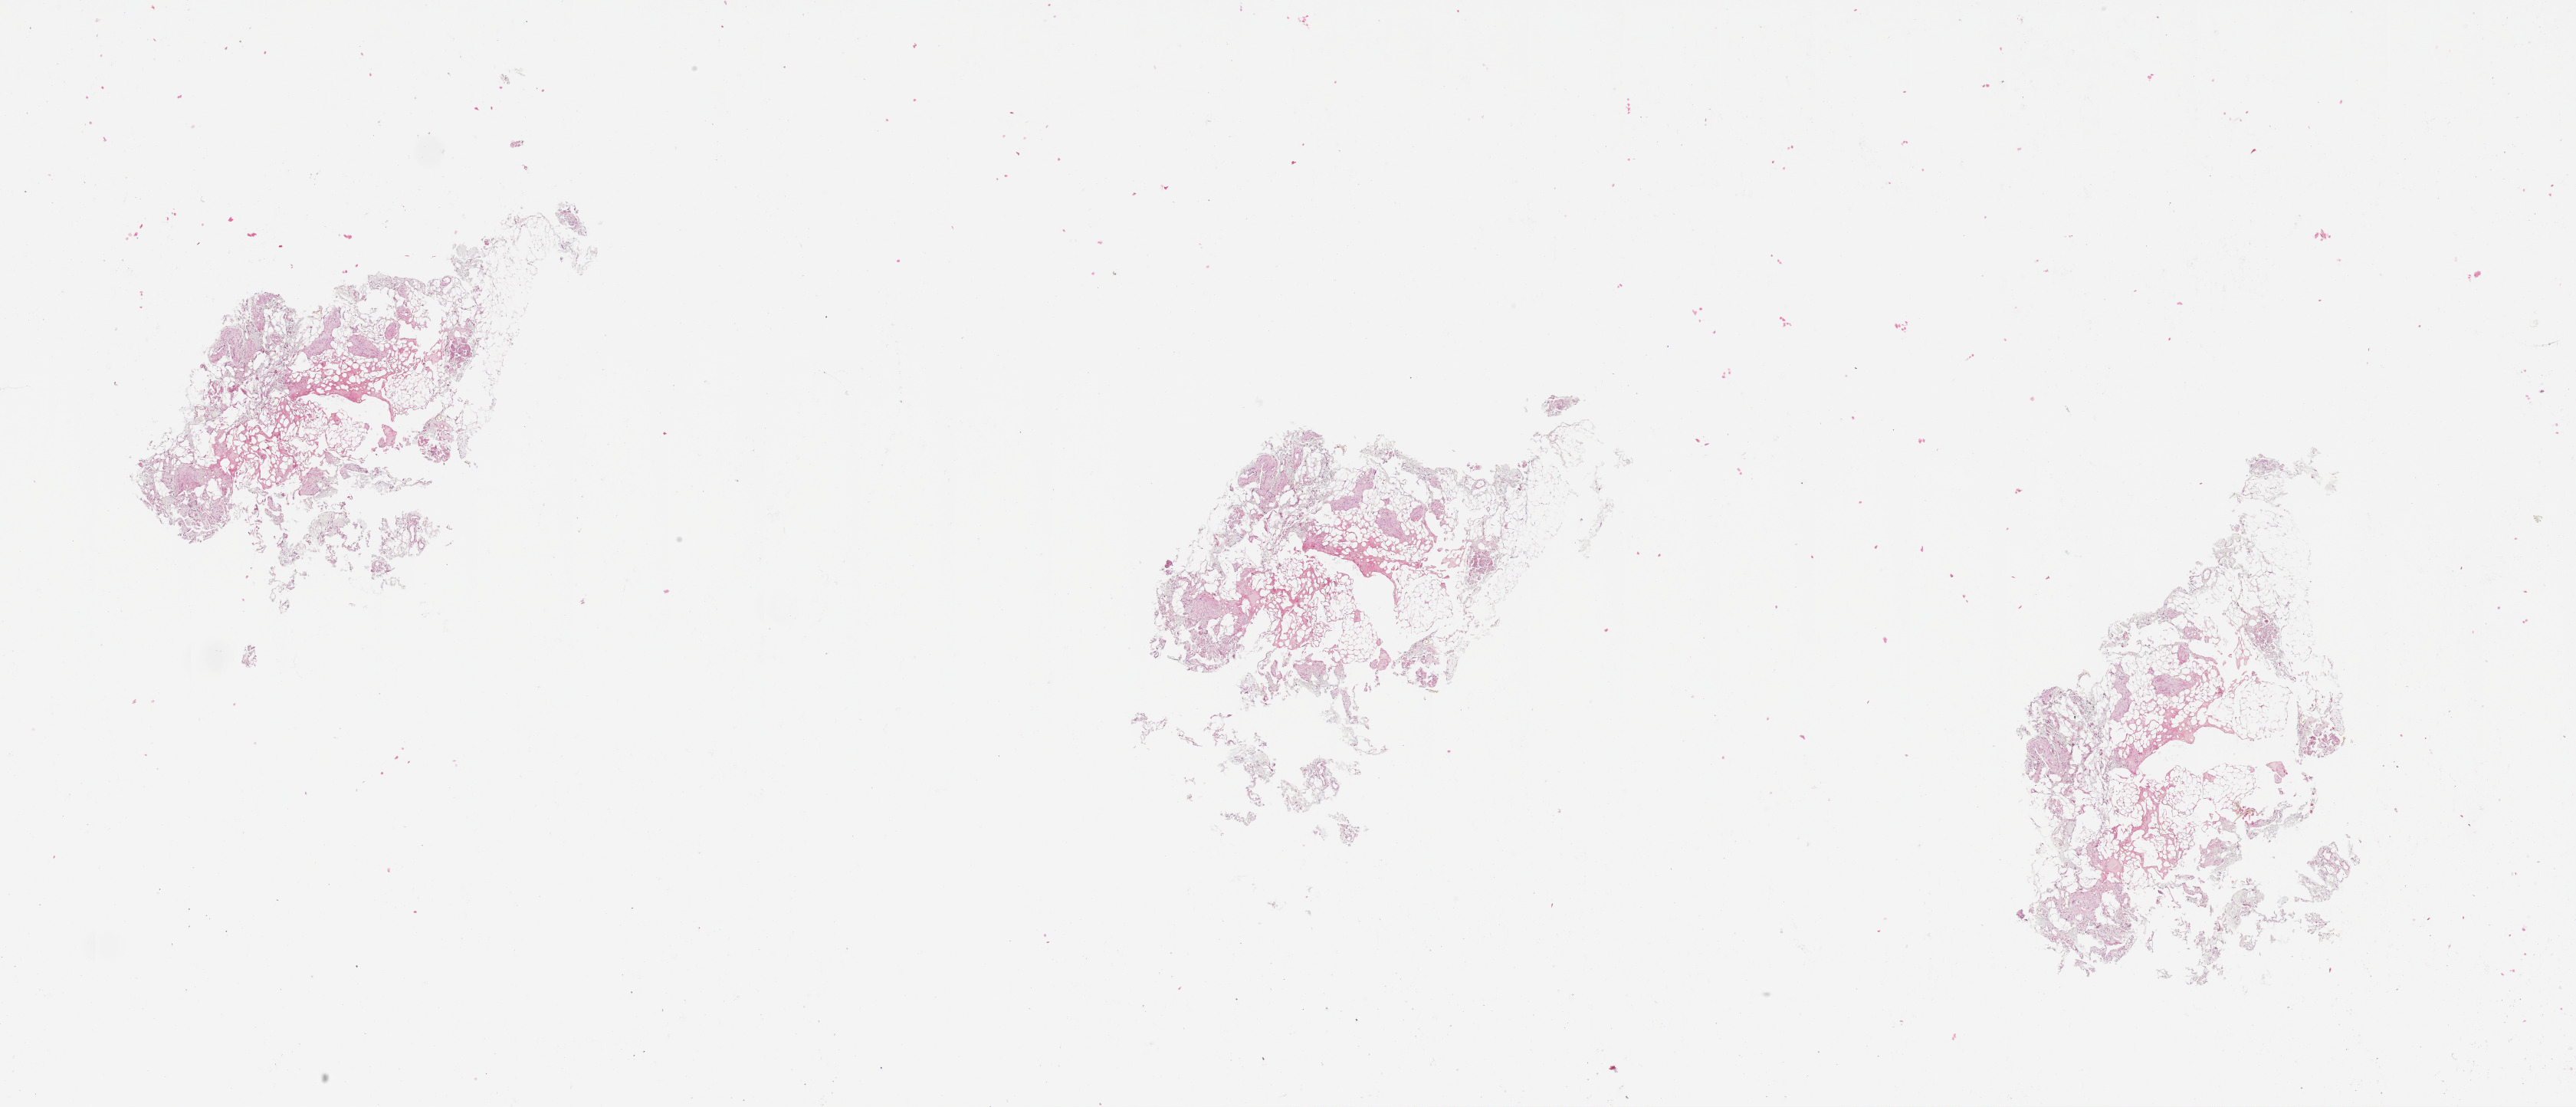
H&E whole-slide image — shown as a low-resolution overview of the whole scanned area (about 27.1 x 11.6 mm, acquisition: 20x scan); normal (non-tumour) tissue sample, sampled site: pancreas. Male, 60 y/o.
- this section: normal (non-tumour) tissue from the same patient
- patient diagnosis: Infiltrating duct carcinoma, NOS